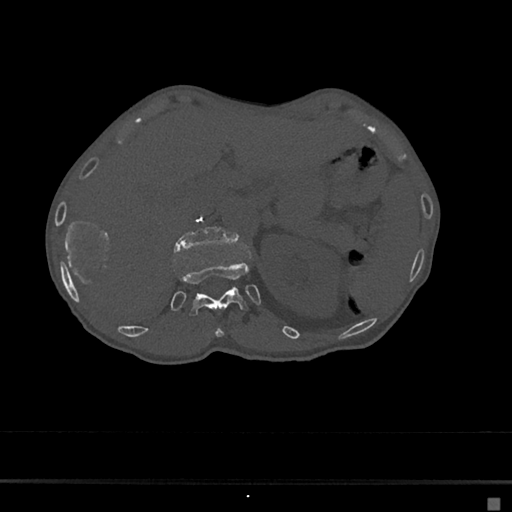
CT including the spine, one axial slice; slice 119 of 797 in the series (ordered by position); reconstruction kernel Br40s/3; 120 kVp; bone window (W 1800 / L 400 HU); 512 × 512 image matrix, field of view 360 × 360 mm. Patient: female, 68 years. Case-level facts recorded for this patient, not image findings: primary cancer: renal.
Annotated regions visible in this slice (semi-automatic segmentation, software-assisted and operator-edited):
- L1 vertebra: bounding box [x1, y1, x2, y2] px = [173, 226, 238, 253]
- T11 vertebra: [215, 328, 224, 338]
- T12 vertebra: [174, 260, 249, 317]